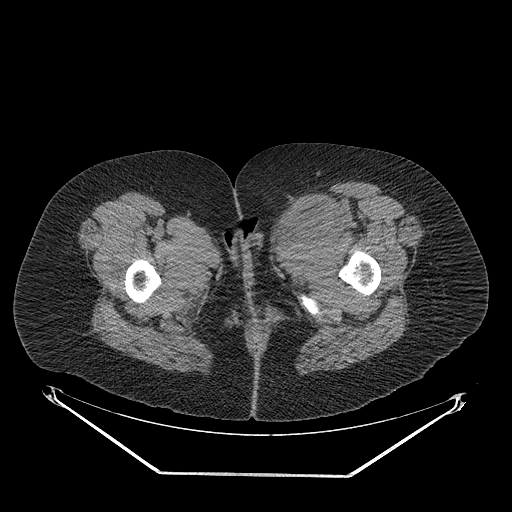
CT of an extremity soft-tissue mass (from a PET/CT study), one axial slice. Position 40 of 267 along the scan axis. 140 kVp. Soft-tissue window (W 400 / L 40 HU). 3.75 mm slice thickness. 512 × 512 image matrix, field of view 500 × 500 mm. Female patient. Case-level facts recorded for this patient, not image findings: histological type: myxofibrosarcoma; grade: intermediate; site of the primary tumour: left thigh.
Annotated regions visible in this slice (expert contour drawn on MRI and transferred to this co-registered scan by the dataset authors):
- gross tumour volume including surrounding oedema: bounding box <265,198,359,254> (left, top, right, bottom; pixels)
- gross tumour volume (mass): <276,198,344,241>